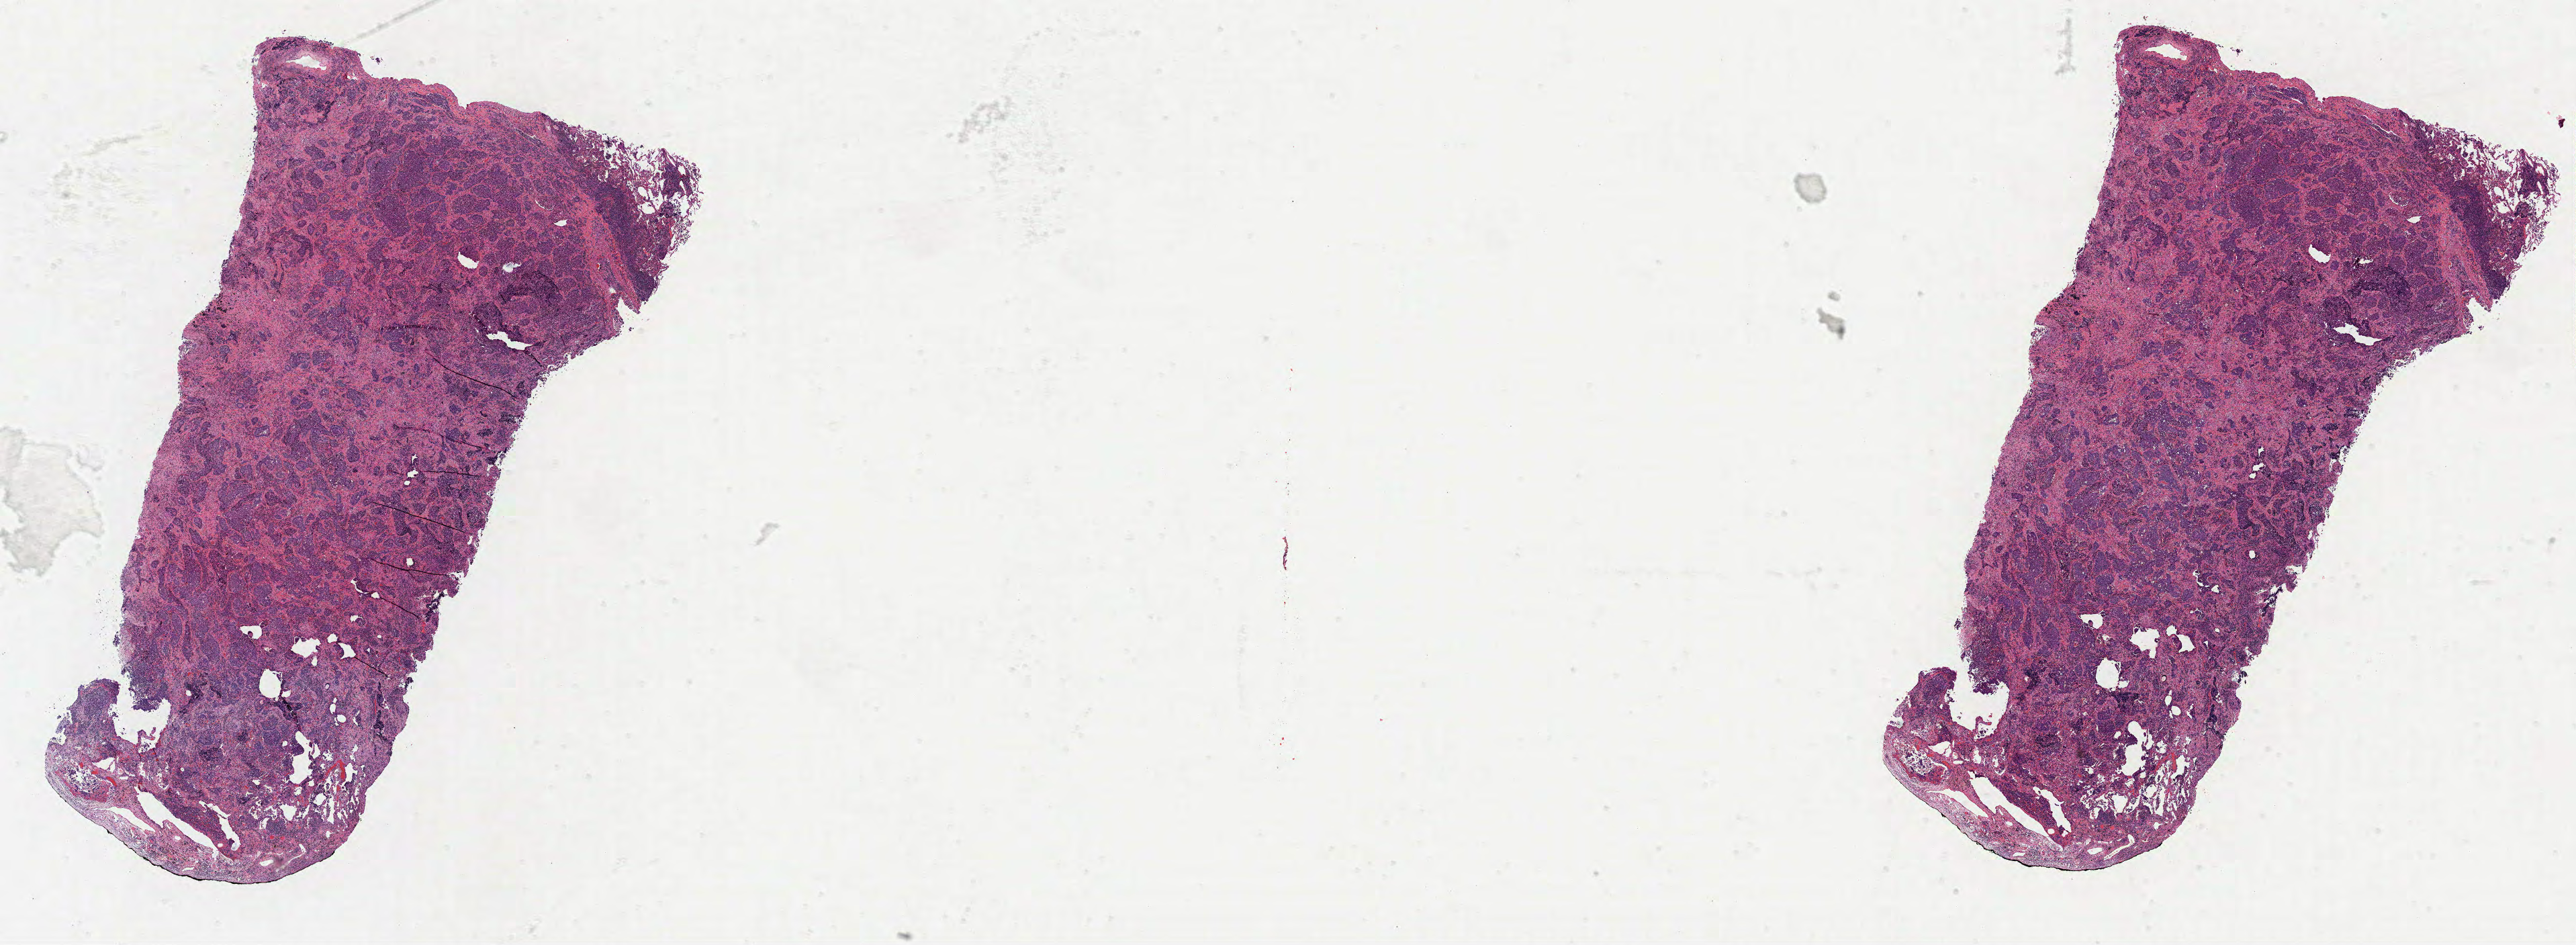
Digitized Hematoxylin and eosin (H&E) stained tissue section (whole slide), shown as a low-resolution overview of the whole scanned area (about 30.9 x 11.3 mm, from a 40x scan), formalin-fixed paraffin-embedded (FFPE) diagnostic section, lung, primary tumour sample. Male patient; age at initial diagnosis 59 years.
• TNM: T1 N0 MX
• histologic diagnosis: Adenocarcinoma, NOS
• AJCC pathologic stage: IA (6th edition)